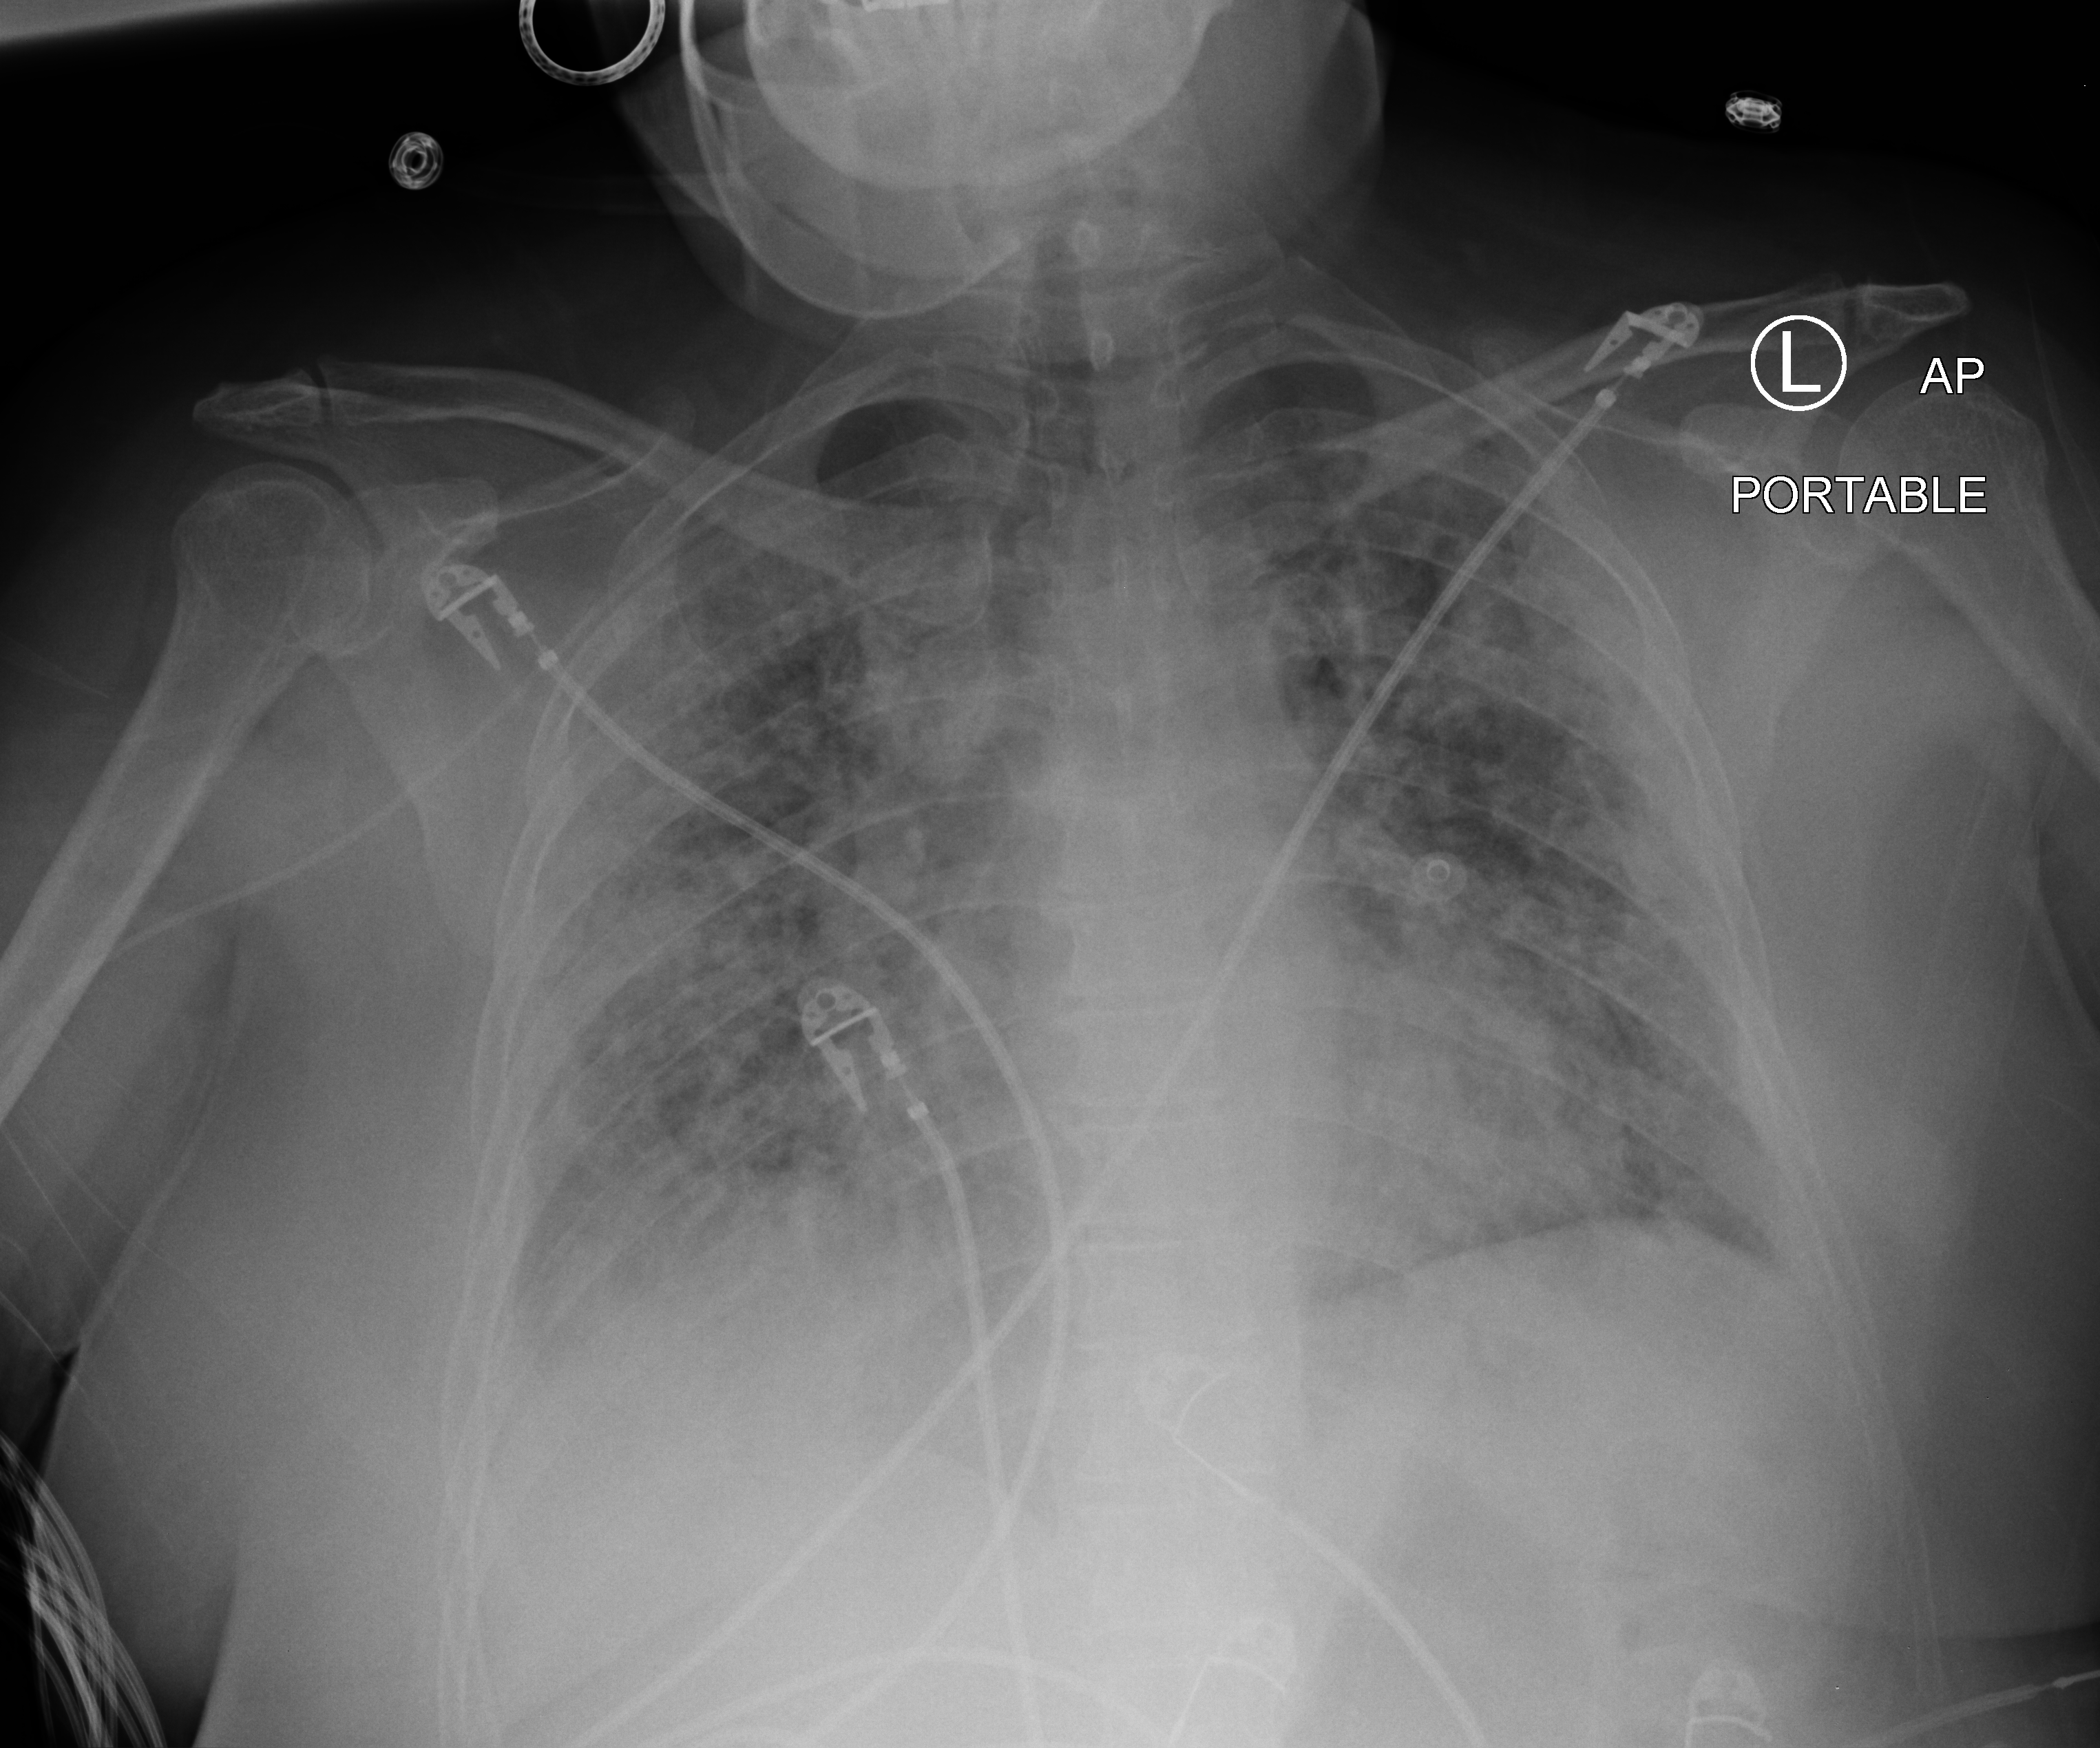
Bedside chest radiograph (computed radiography), anteroposterior (AP) projection. Patient hospitalised with COVID-19; female, aged 18–59 years.
Admission-level facts for this patient (not findings on this image; timing relative to this image not recorded): smoking status (admission record): never; admitted to intensive care during this hospital stay: no; mechanically ventilated during this hospital stay: no.